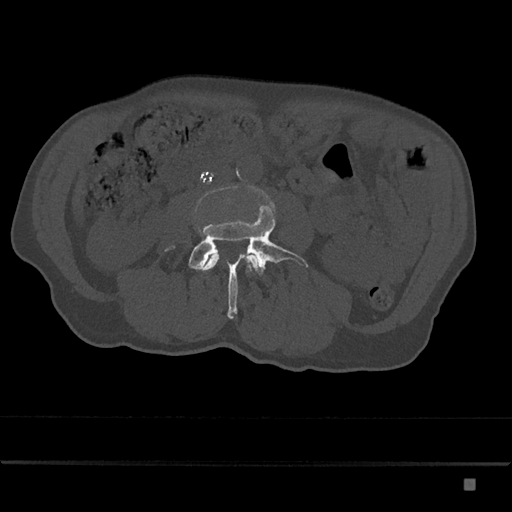
CT including the spine, one axial slice. Slice 359 of 797 in the series (ordered by position). Reconstruction kernel Br40s/3. 120 kVp. Bone window (W 1800 / L 400 HU). 0.5 mm slice thickness. 512 × 512 image matrix, field of view 390 × 390 mm. Patient: male, 72 years. From the clinical record (not read from this slice): primary cancer: prostate.
Structures marked on this image (semi-automatically segmented with operator editing):
- L3 vertebra: bounding box [x1, y1, x2, y2] px = [203, 253, 259, 271]
- L4 vertebra: [165, 205, 308, 319]